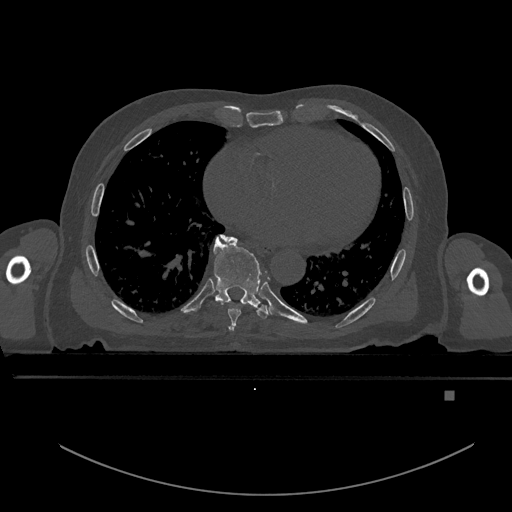
CT including the spine, one axial slice; slice 223 of 969 in the series (ordered by position); bone window (W 1800 / L 400 HU); 0.5 mm slice thickness; 512 × 512 image matrix. Patient: male, 82 years. Case-level facts recorded for this patient, not image findings: primary cancer: prostate.
Annotated regions visible in this slice (semi-automatically segmented with operator editing):
- T6 vertebra: box from (x=228, y=326) to (x=233, y=332) px
- T7 vertebra: (x=221, y=235)–(x=241, y=326)
- T8 vertebra: (x=213, y=236)–(x=271, y=319)